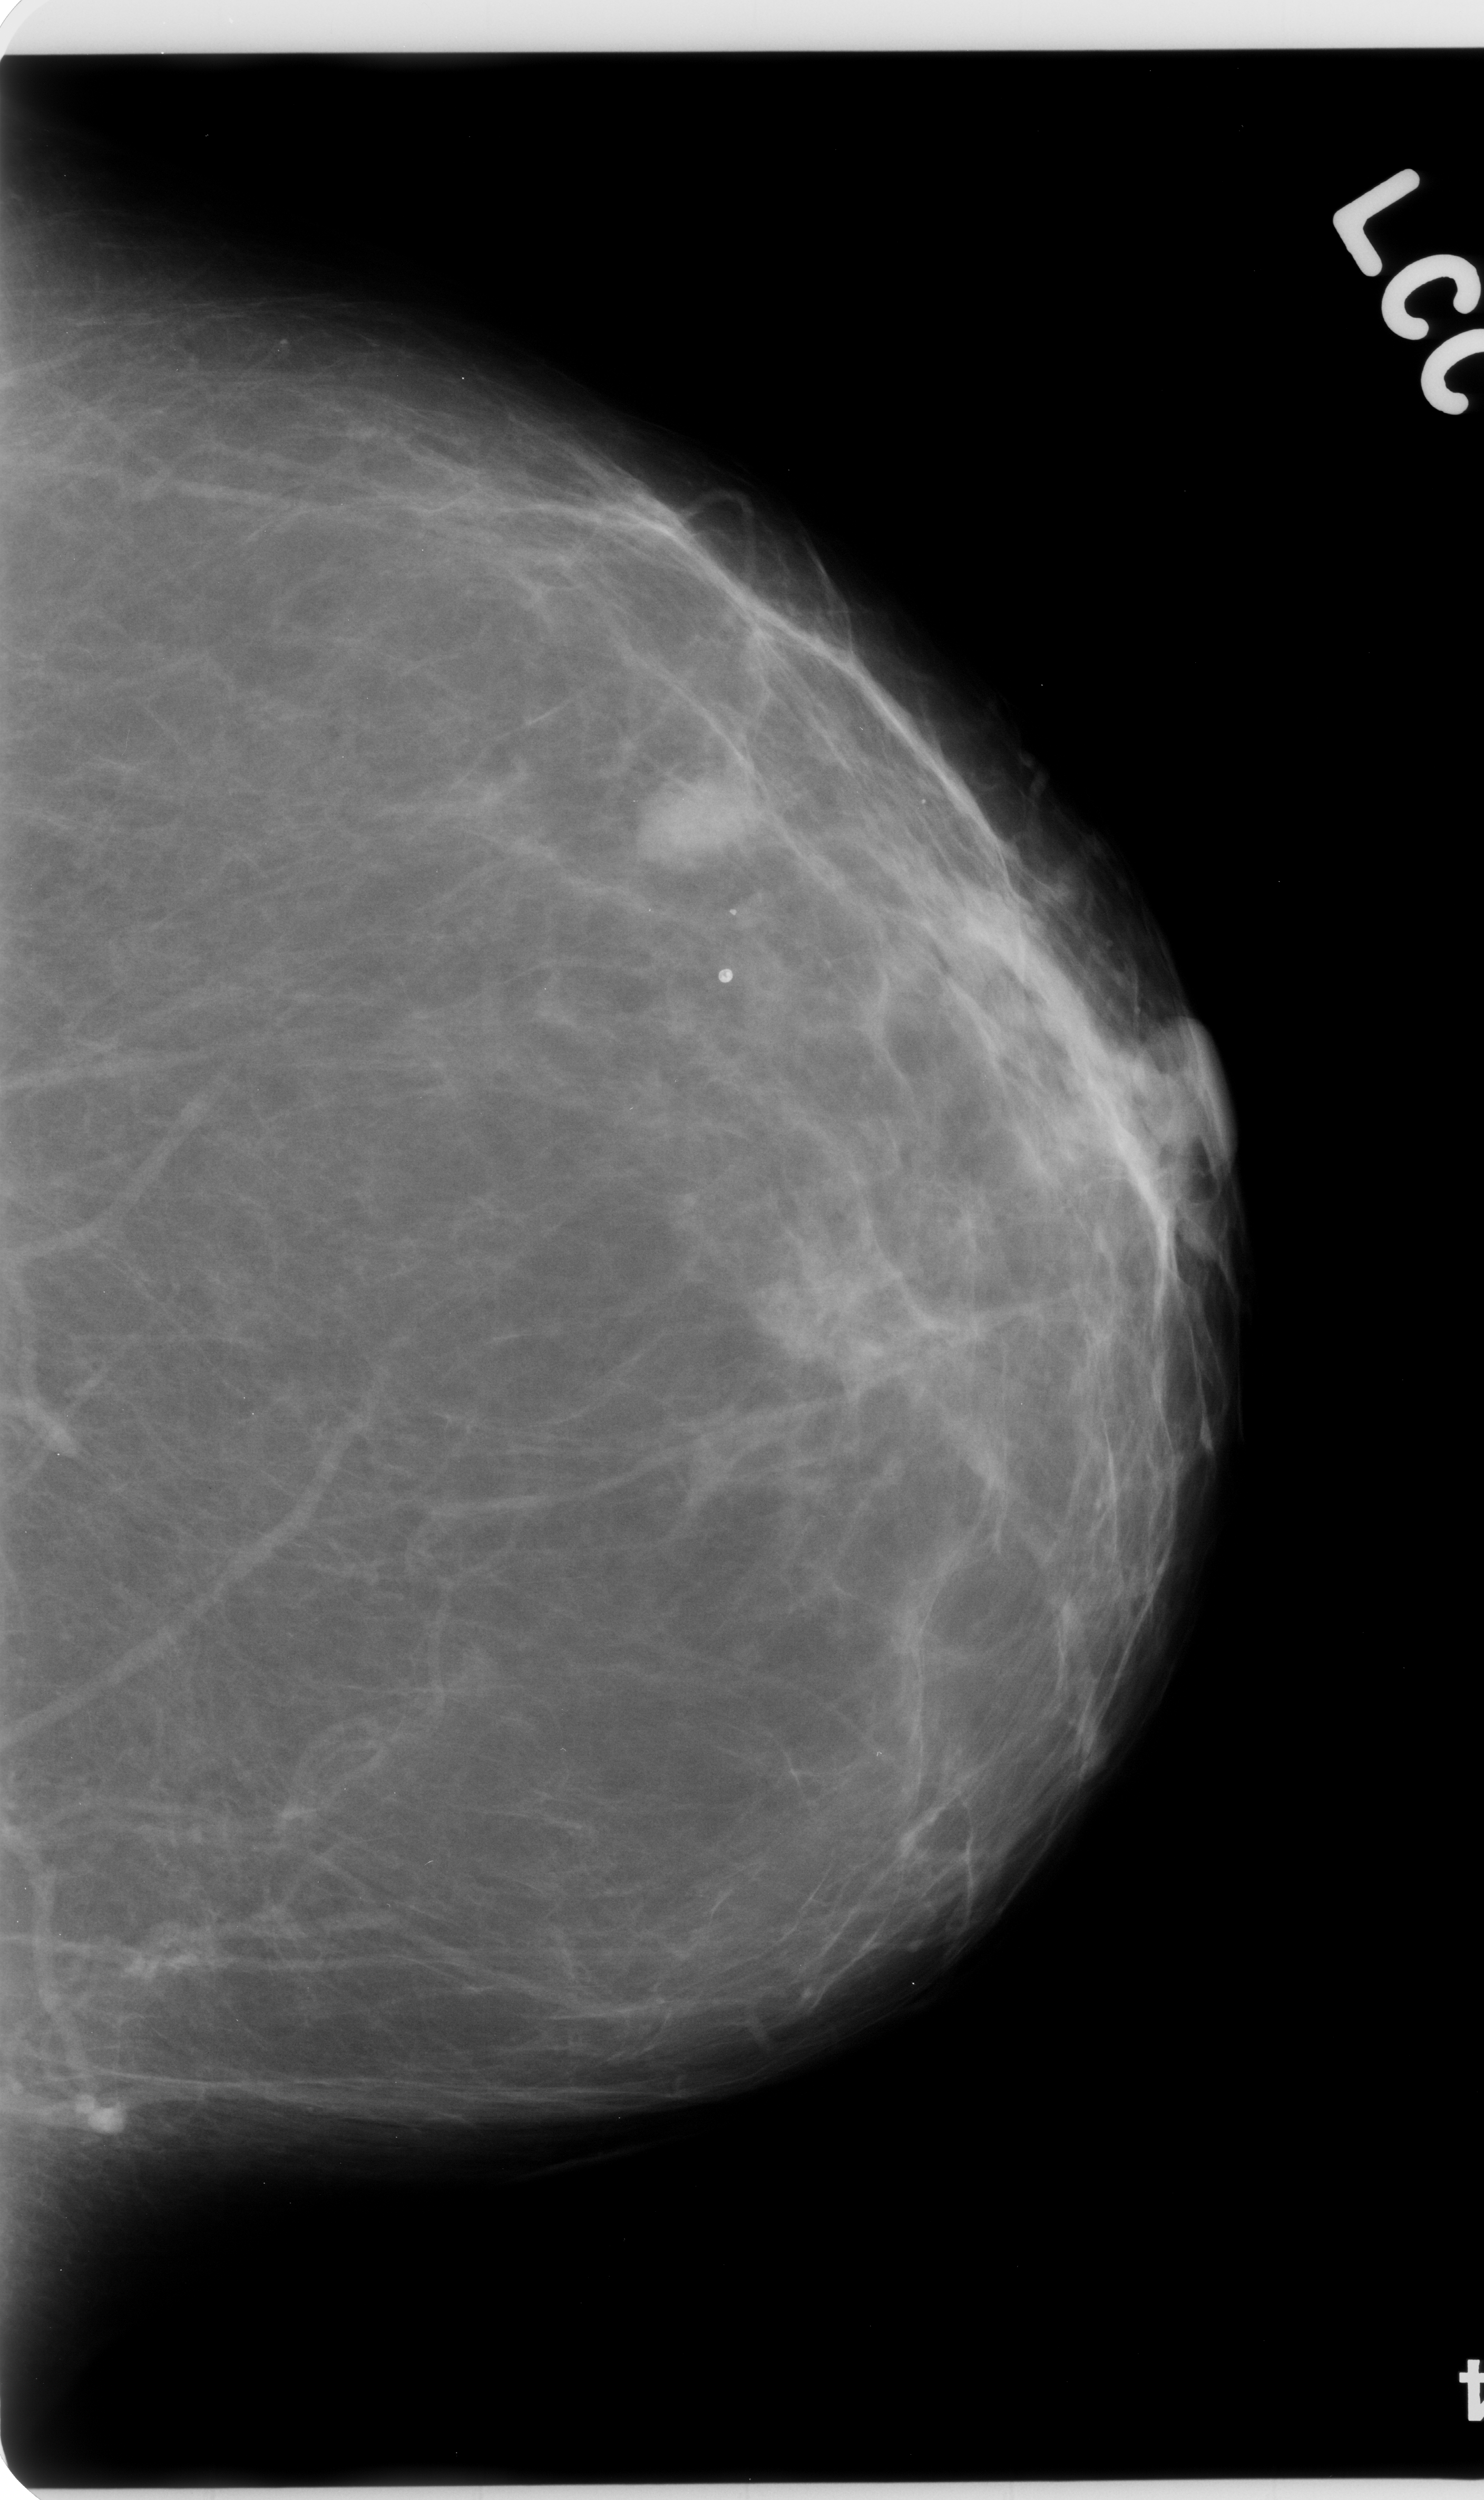
Digitized screen-film mammogram. Left breast. Craniocaudal (CC) view. BI-RADS breast density category 1 (scale 1–4). 1484 × 2500 image matrix.
Marked abnormalities (boxes around the expert regions of interest):
- mass, shape oval, margins microlobulated; BI-RADS assessment category 4; pathology result (as recorded, not read from the image): malignant: bounding box [x1, y1, x2, y2] px = [635, 779, 748, 886]